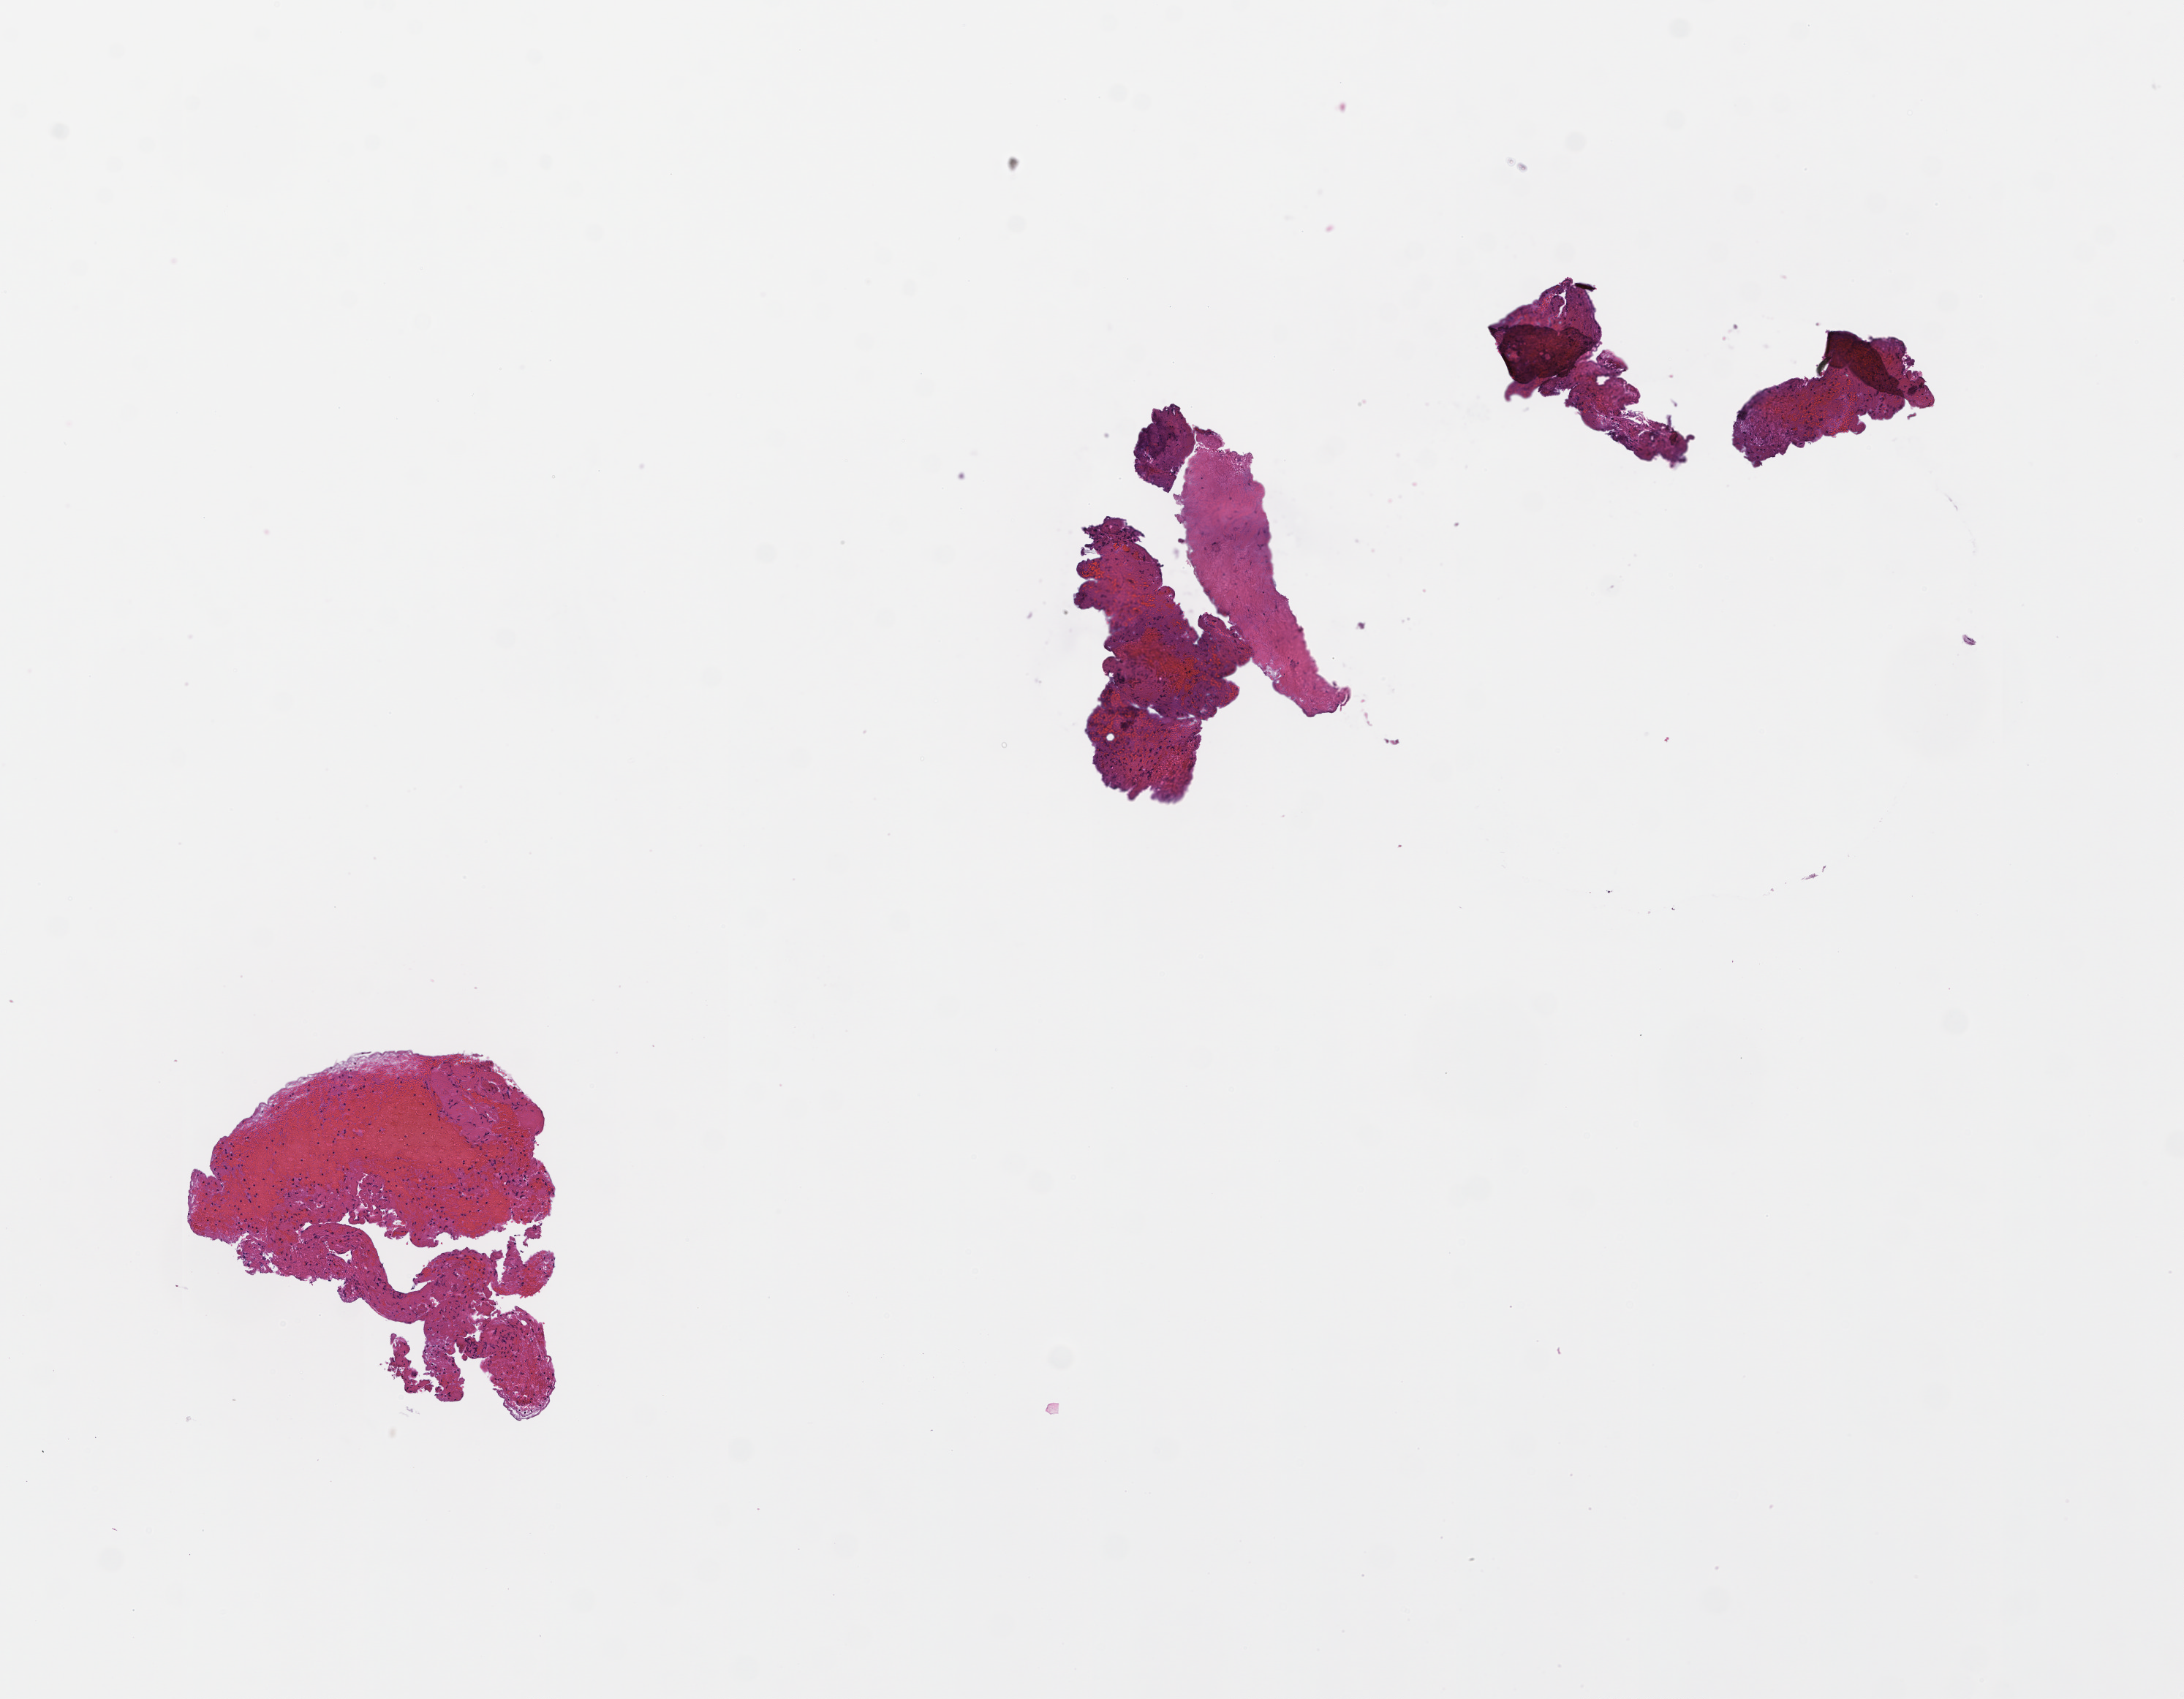
Whole-slide image, hematoxylin and eosin (H&E) stain, shown as a low-resolution overview of the whole scanned area (about 6.0 x 4.7 mm). Formalin-fixed, paraffin-embedded (FFPE) tissue. Collected at disease progression. Female patient.
• this section: metastasis (sampled organ not recorded)
• primary diagnosis of the patient: Non-Small Cell Lung Carcinoma